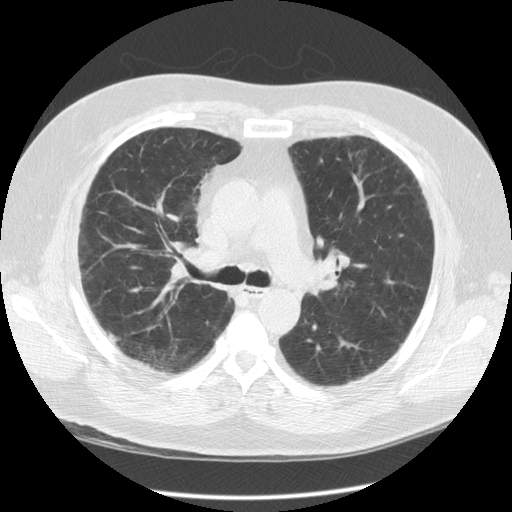
Low-dose screening chest CT, axial slice. Second screening round (one year after baseline). Lung window (W 1500 / L -600 HU). 2.5 mm slice thickness. Standard (soft-tissue) reconstruction kernel (STANDARD). 512 × 512 image matrix. Male participant, aged 56 years at enrolment.
Lesion marked by an expert reader, box from (x=97, y=321) to (x=129, y=353) px. The exam's reader record, not a measurement of the box and not confirmed to be the same lesion: non-calcified nodule or mass ≥4 mm, right upper lobe, 7 × 5 mm, poorly defined margins, soft tissue attenuation, pre-existing on the prior screen: no. Later outcome: lung cancer diagnosed 399 days after this screen — large cell neuroendocrine carcinoma, right upper lobe, stage IIIA (AJCC 6th edition), 10 mm at pathology.